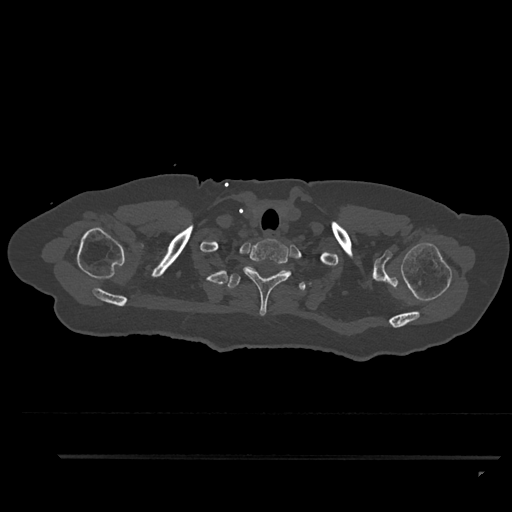
CT including the spine, one axial slice; position 753 of 797 along the scan axis; reconstruction kernel Br40s/3; bone window (W 1800 / L 400 HU); 0.5 mm slice thickness; 512 × 512 image matrix, field of view 408 × 408 mm. Patient: female, 44 years. Case-level facts recorded for this patient, not image findings: primary cancer: renal.
Outlined on this slice (semi-automatically segmented with operator editing):
- T1 vertebra: bounding box <243,239,291,316> (left, top, right, bottom; pixels)
- T2 vertebra: <227,273,306,291>